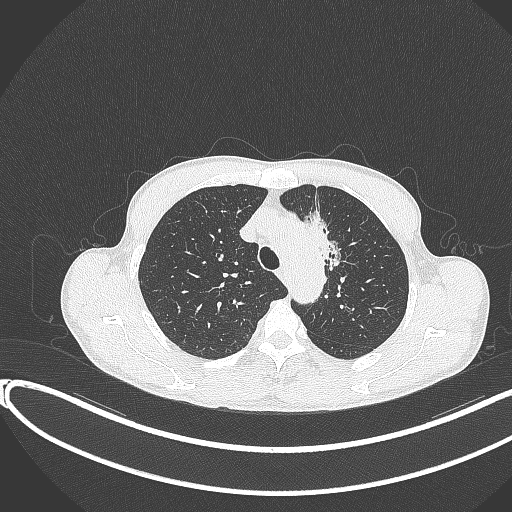
Chest CT, one axial slice; slice 292 of 374 in the series (ordered by position); lung window (W 1500 / L -600 HU); 1 mm slice thickness; 512 × 512 image matrix, field of view 400 × 400 mm. Patient: male, 58 years. From the clinical record (not read from this slice): clinical TNM (as recorded): T1c N1 M0.
Structures marked on this image (bounding box drawn by a radiologist):
- lung tumour (recorded histology: adenocarcinoma): box from (x=297, y=209) to (x=351, y=277) px